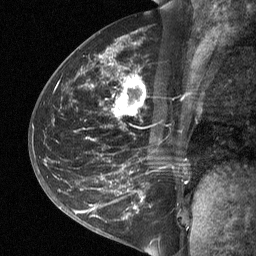
Breast MRI (dynamic contrast-enhanced), one sagittal slice. Slice 30 of 64 in the series (ordered by position). Dynamic contrast-enhanced study with each time point stored as its own series, time point 2 of 3 at this slice position (early post-contrast, ordered by acquisition time). 1.5 T. TE 4.8 ms, TR 27 ms. 2 mm slice thickness. 256 × 256 image matrix, field of view 200 × 200 mm. Patient: female, 42 years. From the clinical record (not read from this slice): setting: breast cancer imaged before/during neoadjuvant chemotherapy; receptor status: triple-negative.
Outlined on this slice (semi-automatic segmentation, software-assisted and operator-edited):
- analysis volume of interest (the breast-tissue region the enhancement analysis was run in; not a lesion): bounding box [x1, y1, x2, y2] px = [49, 45, 197, 197]
- tumour enhancement mask (voxels above the 90 % enhancement threshold inside the analysis volume of interest): [118, 78, 137, 107]